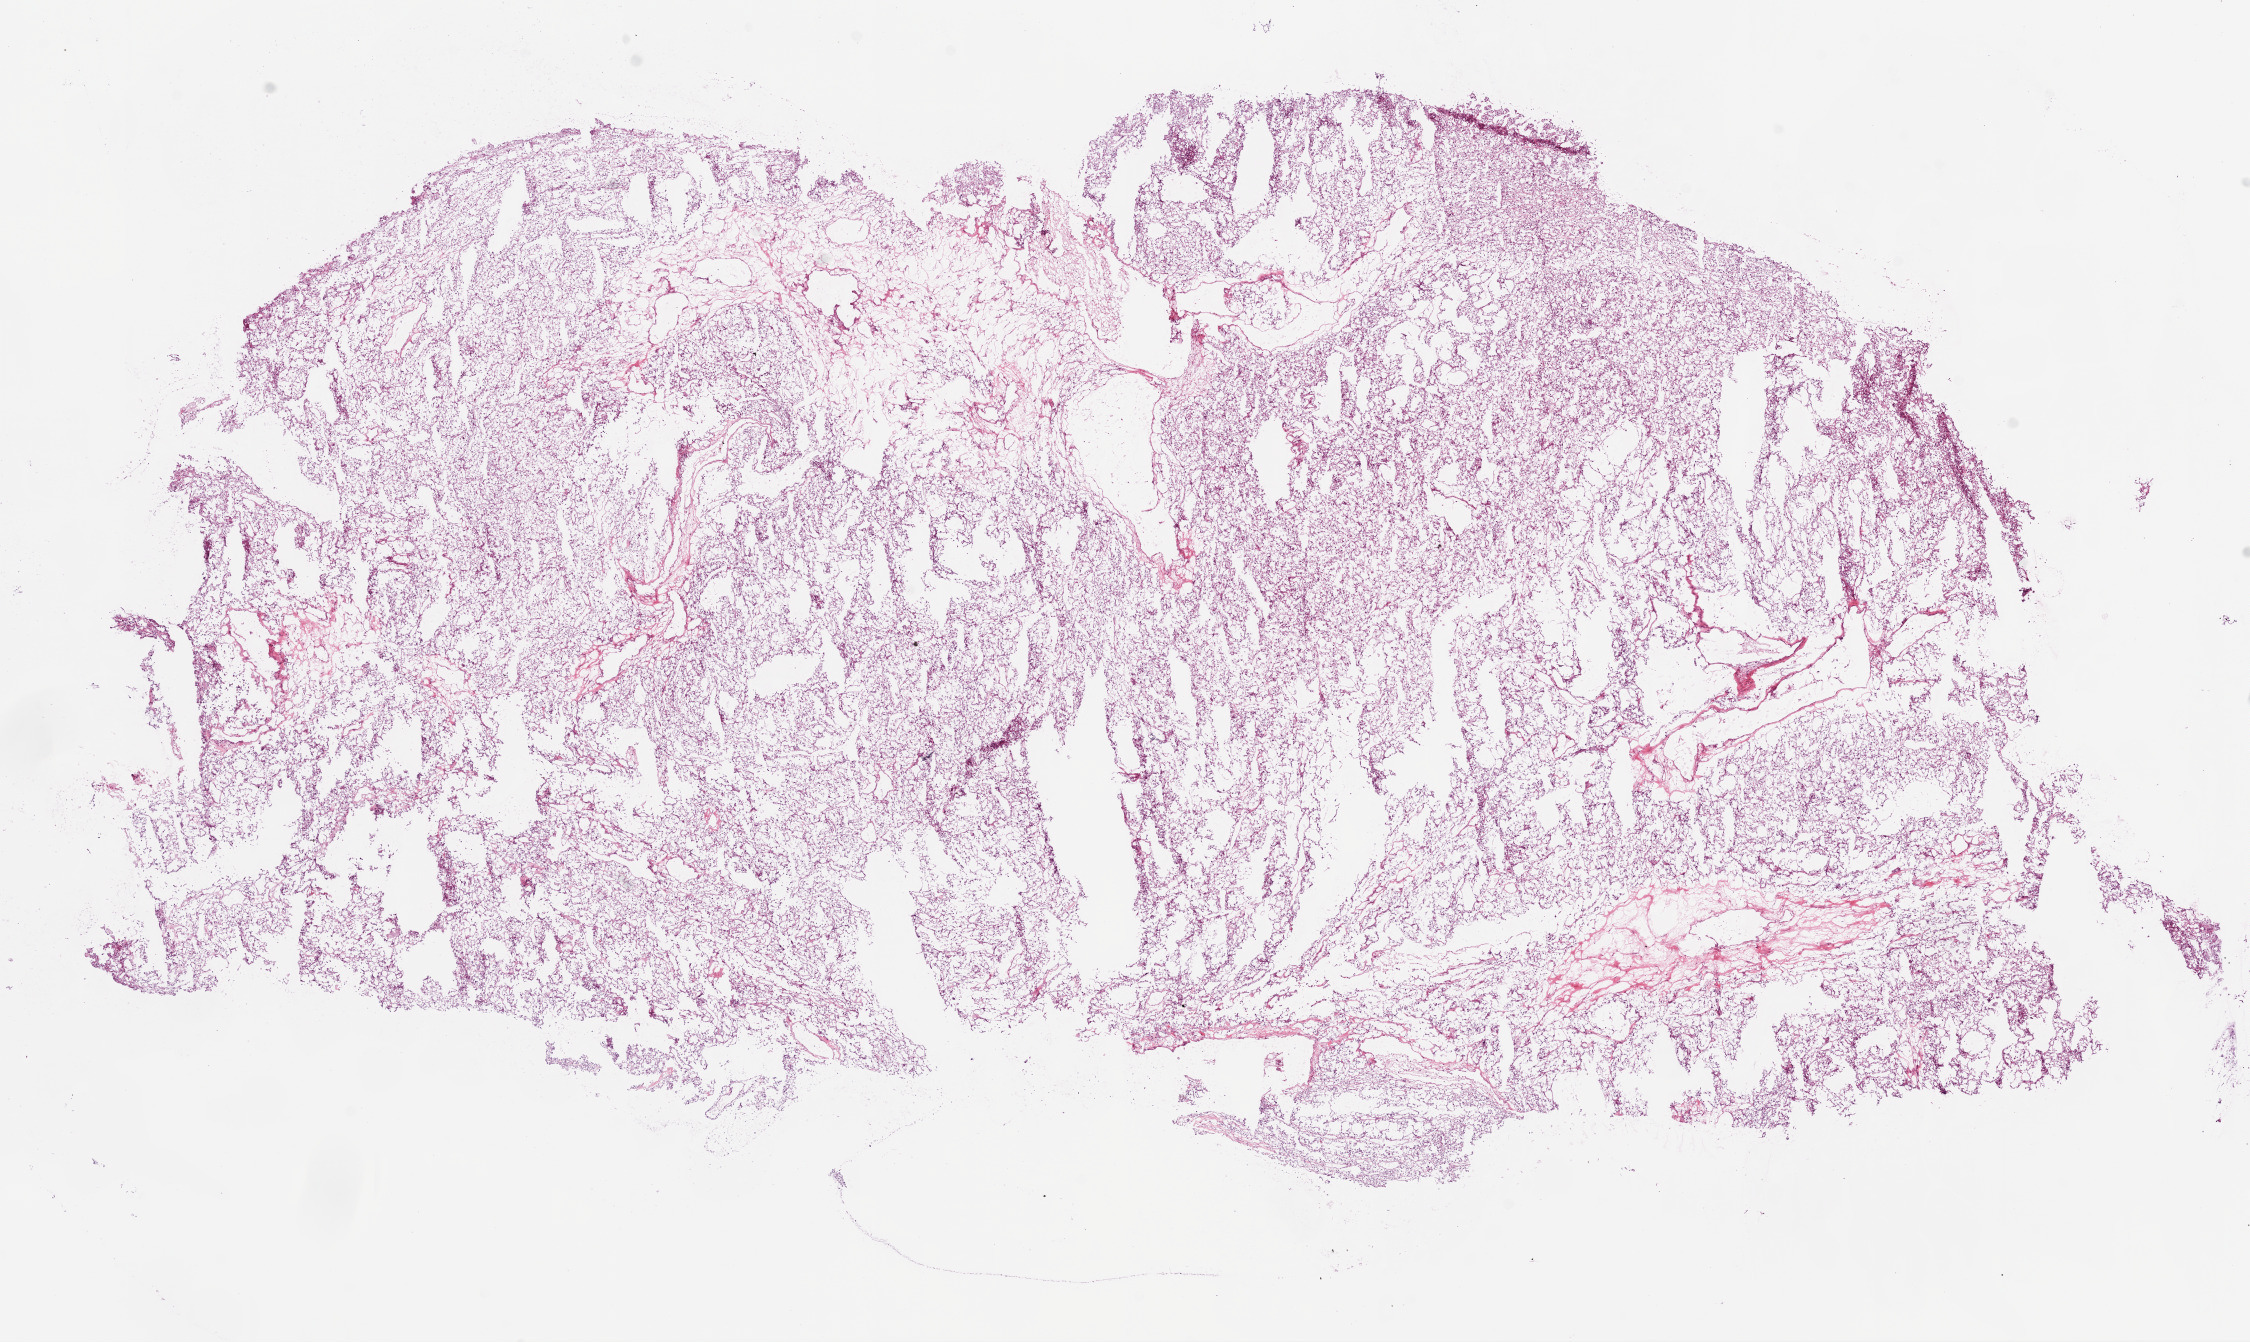
Whole-slide histology image, H&E — whole scanned area (about 18.1 x 10.8 mm) shown as a low-resolution overview. Frozen section. Sample: primary tumour, kidney. Male patient; age at initial diagnosis 52 years. Histologic grade: G3 (poorly differentiated). Slide review estimates, as recorded: tumour cells 90%, tumour nuclei 85%, normal cells 0%, stromal cells 10%, necrosis 0%.
• diagnosis: Clear cell adenocarcinoma, NOS
• AJCC pathologic stage: III (7th edition)